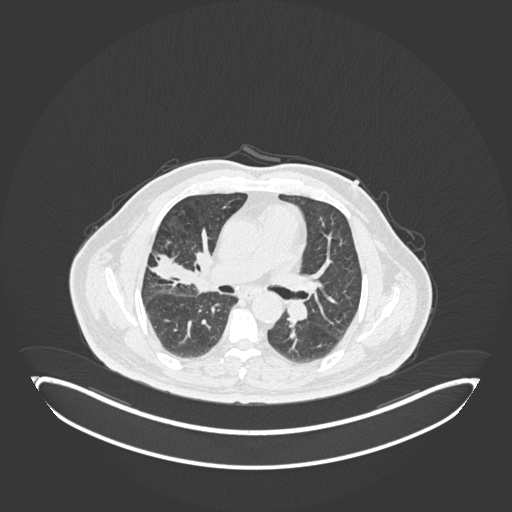
Chest CT, one axial slice; slice 94 of 247 in the series (ordered by position); reconstruction kernel B30f; lung window (W 1500 / L -600 HU); 512 × 512 image matrix, field of view 500 × 500 mm. Patient: male, 72 years. Case-level facts recorded for this patient, not image findings: clinical TNM (as recorded): T1c N0 M0.
Structures marked on this image (rectangle marked by the reading radiologist):
- lung tumour (recorded histology: squamous cell carcinoma): box from (x=177, y=242) to (x=212, y=296) px